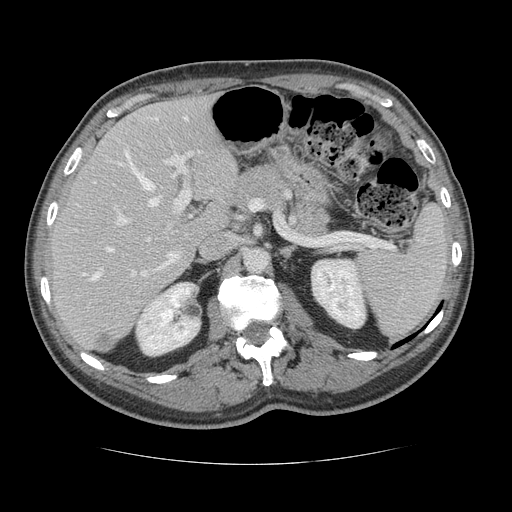
Contrast-enhanced abdominal CT, one axial slice; slice 80 of 134 in the series (ordered by position); 120 kVp; intravenous contrast given; soft-tissue window (W 400 / L 40 HU); 512 × 512 image matrix, field of view 377 × 377 mm. Male patient, age 68 years. Case-level facts recorded for this patient, not image findings: diagnosis: colorectal cancer liver metastases, imaged before liver resection; multiple liver metastases: yes; largest metastasis: 2.2 cm; chemotherapy before resection: no.
Annotated regions visible in this slice (outlined manually by an expert reader):
- hepatic veins: box from (x=83, y=118) to (x=159, y=280) px
- liver: (x=50, y=96)–(x=238, y=352)
- planned liver remnant (the part of the liver to remain after resection): (x=51, y=96)–(x=238, y=339)
- portal vein (with intrahepatic branches): (x=114, y=116)–(x=194, y=276)
- liver metastasis: (x=96, y=333)–(x=116, y=350)